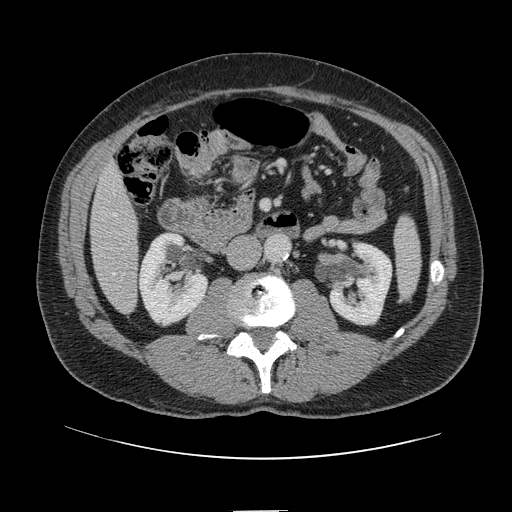
Contrast-enhanced abdominal CT, one axial slice; position 27 of 161 along the scan axis; intravenous contrast given; soft-tissue window (W 400 / L 40 HU); 2.5 mm slice thickness; 512 × 512 image matrix. Male patient, age 66 years. Case-level facts recorded for this patient, not image findings: diagnosis: colorectal cancer liver metastases, imaged before liver resection; multiple liver metastases: no; largest metastasis: 3.5 cm.
Structures marked on this image (outlined manually by an expert reader):
- hepatic veins: bounding box <113,213,116,275> (left, top, right, bottom; pixels)
- liver: <92,167,139,313>
- planned liver remnant (the part of the liver to remain after resection): <92,167,137,257>